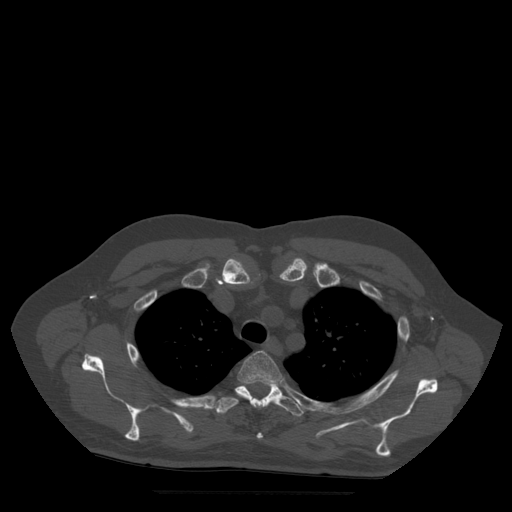
CT including the spine, one axial slice. Position 400 of 522 along the scan axis. Bone window (W 1800 / L 400 HU). 1.25 mm slice thickness. 512 × 512 image matrix. Patient age 72 years. Case-level facts recorded for this patient, not image findings: primary cancer: prostate.
Structures marked on this image (semi-automatic segmentation, software-assisted and operator-edited):
- T3 vertebra: bounding box <238,351,282,439> (left, top, right, bottom; pixels)
- T4 vertebra: <215,383,304,416>